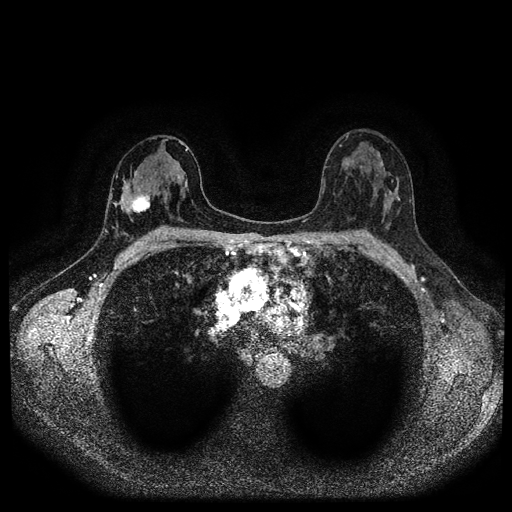
Breast MRI (dynamic contrast-enhanced, multi-phase), one axial slice. Position 59 of 116 along the scan axis. Dynamic contrast-enhanced series, time point 2 of 5 at this slice position (early post-contrast). 1.5 T. TE 2.7 ms, TR 5.4 ms. 512 × 512 image matrix, field of view 330 × 330 mm. Patient: female, 42 years.
Structures marked on this image (semi-automatically segmented with operator editing):
- breast lesion (labelled 'tumour' in the annotation; benign lesions carry a separate 'benign' label): bounding box <128,193,151,216> (left, top, right, bottom; pixels)